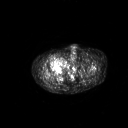
FDG PET of an extremity soft-tissue mass (from a PET/CT study), one axial slice. Position 290 of 311 along the scan axis. 3.27 mm slice thickness. 128 × 128 image matrix, field of view 700 × 700 mm. Male patient, age 50 years. From the clinical record (not read from this slice): histological type: undifferentiated - pleiomorphic; grade: high; site of the primary tumour: right thigh.
Outlined on this slice (expert contour drawn on MRI and transferred to this co-registered scan by the dataset authors):
- gross tumour volume including surrounding oedema: box from (x=56, y=56) to (x=64, y=62) px
- gross tumour volume (mass): (x=56, y=58)–(x=61, y=62)